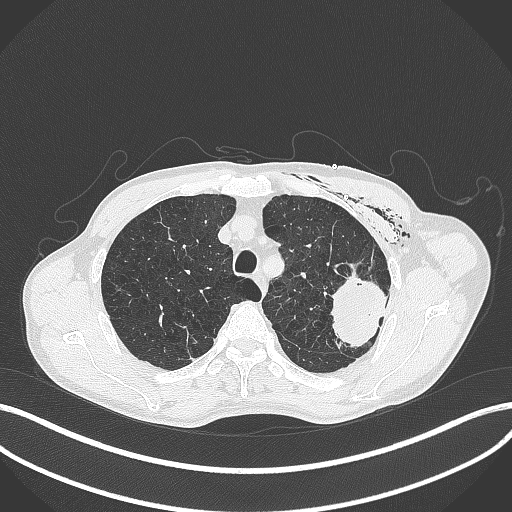
Chest CT, one axial slice; position 321 of 457 along the scan axis; reconstruction kernel B70f; 120 kVp; lung window (W 1500 / L -600 HU); 1 mm slice thickness; 512 × 512 image matrix, field of view 400 × 400 mm. Patient: male, 58 years. From the clinical record (not read from this slice): clinical TNM (as recorded): T3 N0 M0.
Annotated regions visible in this slice (rectangle marked by the reading radiologist):
- lung tumour (recorded histology: adenocarcinoma): bounding box (x1, y1, x2, y2) in pixels: (324, 269, 389, 353)